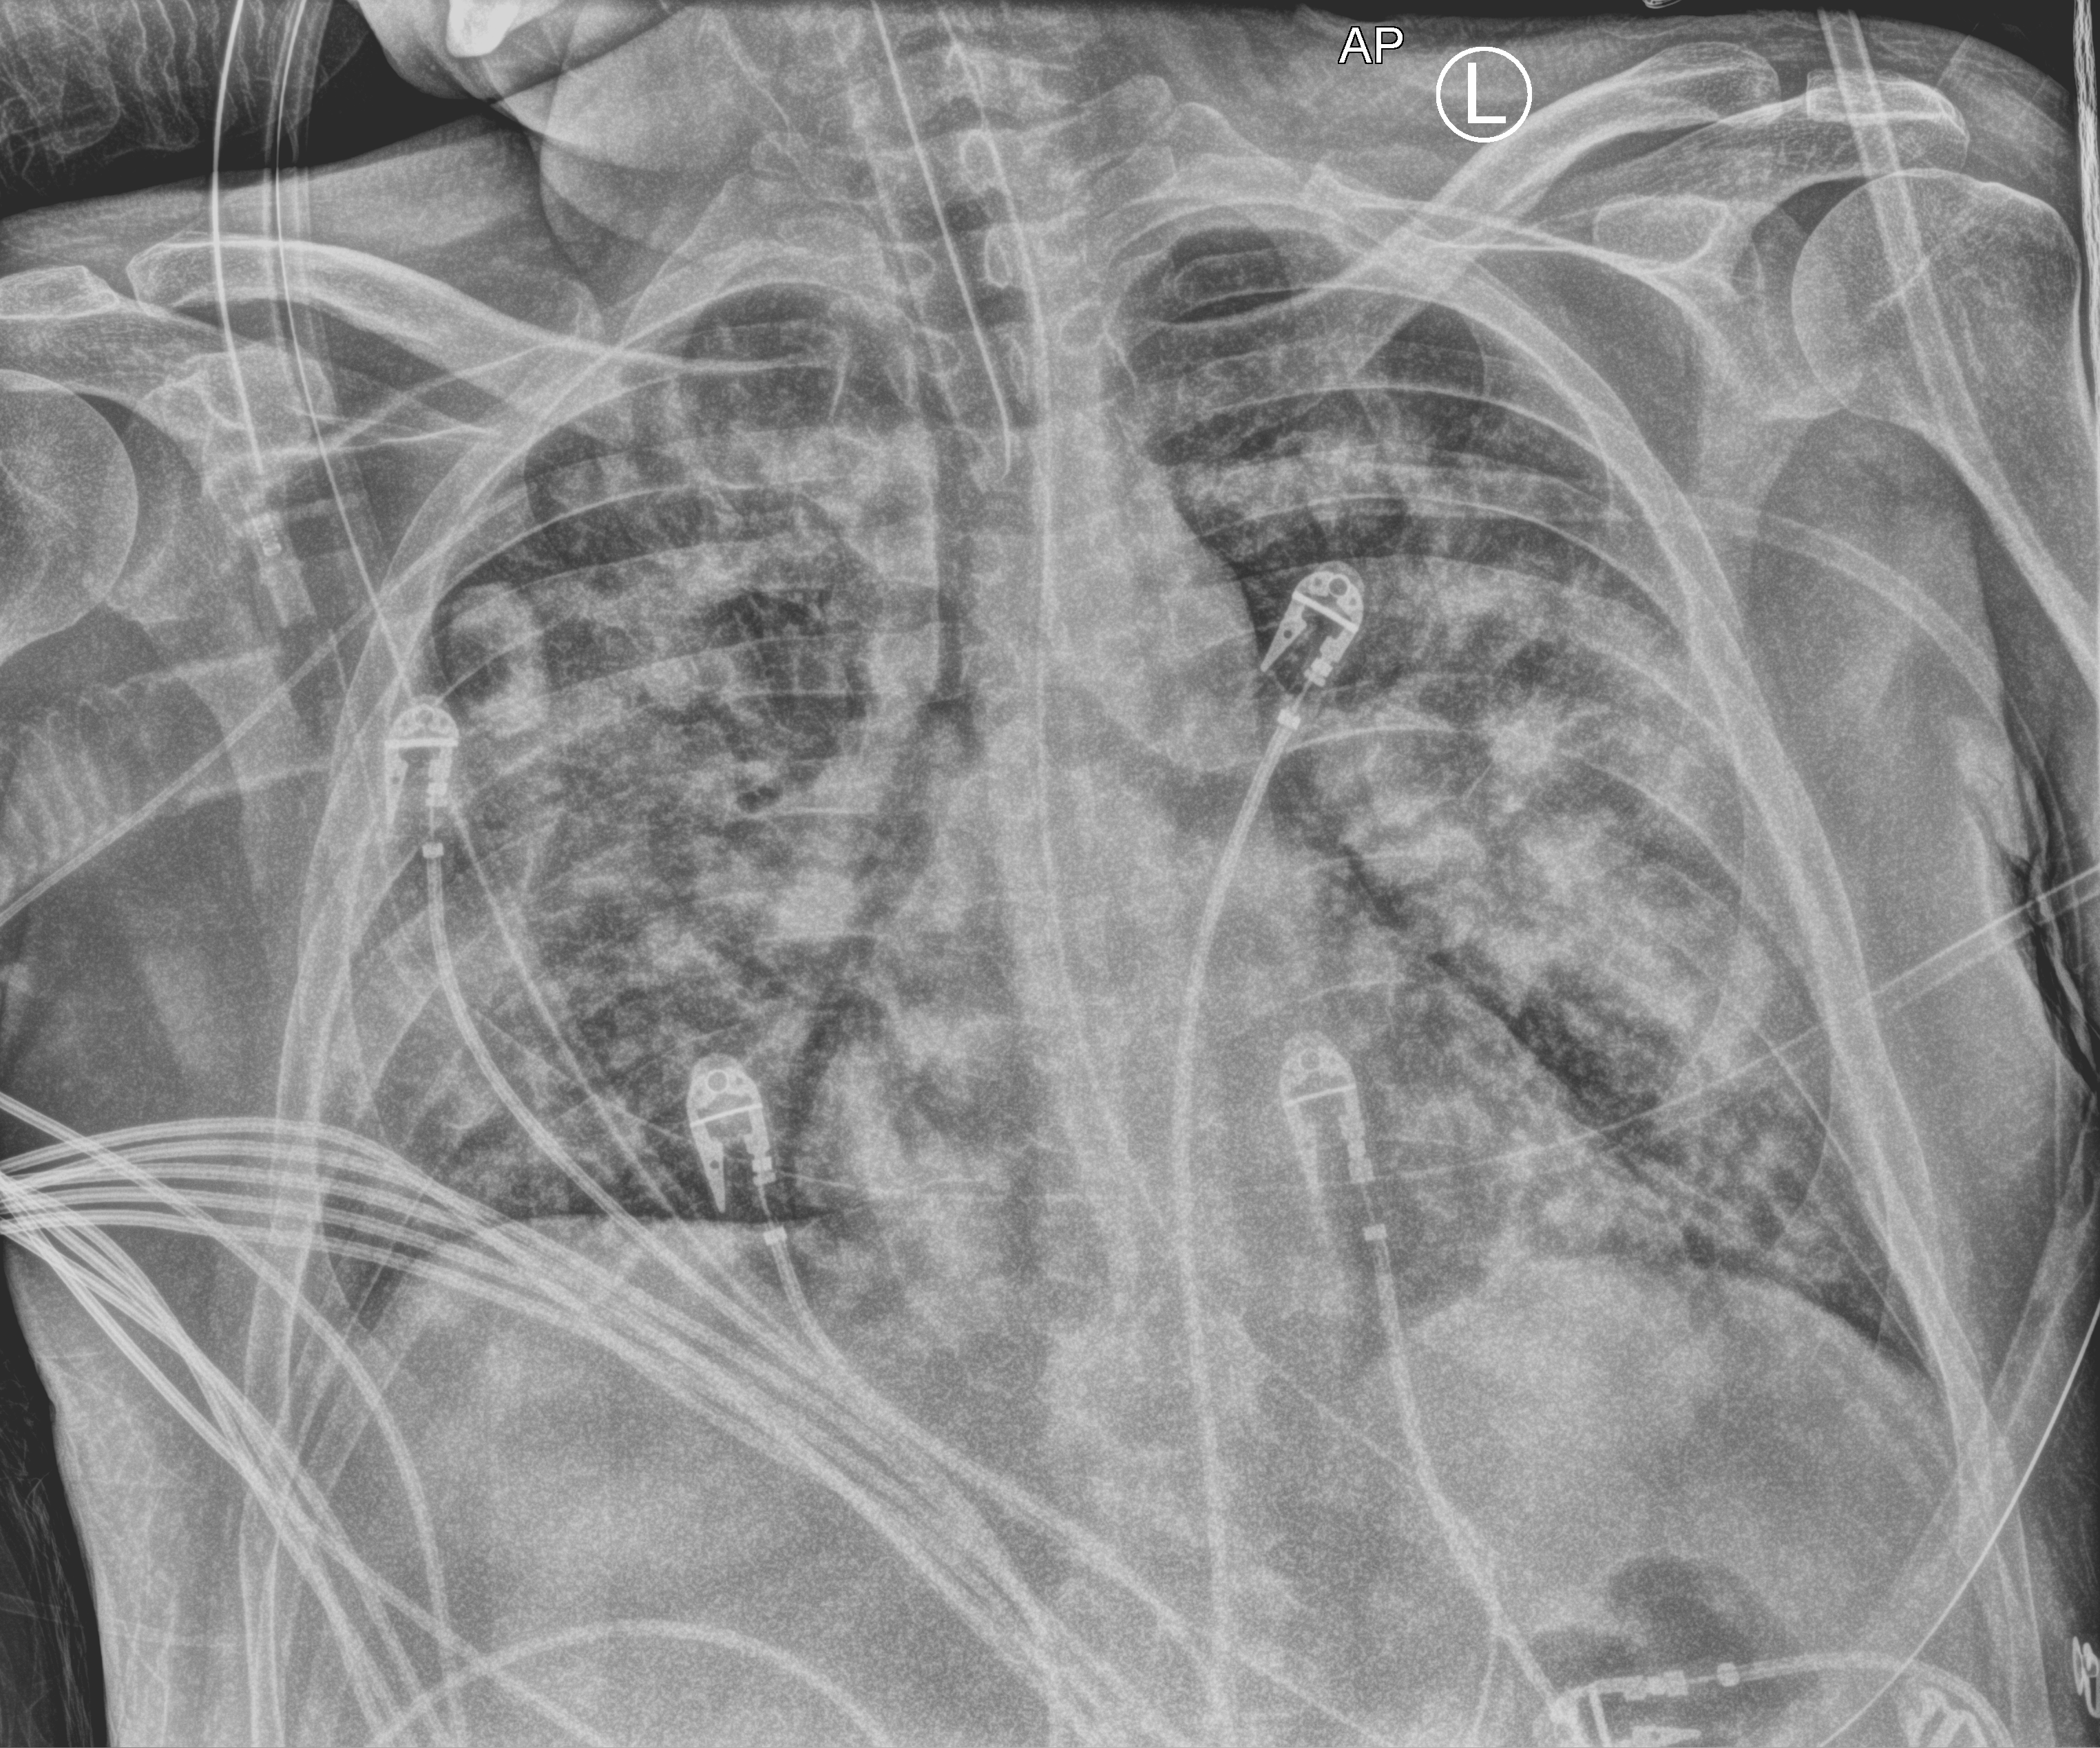
Portable chest radiograph, anteroposterior (AP) projection. Male patient hospitalised with COVID-19, age 18–59 years.
Hospital-stay facts (about this admission, not read from this image; timing relative to this image not recorded): diabetes (admission record): yes.